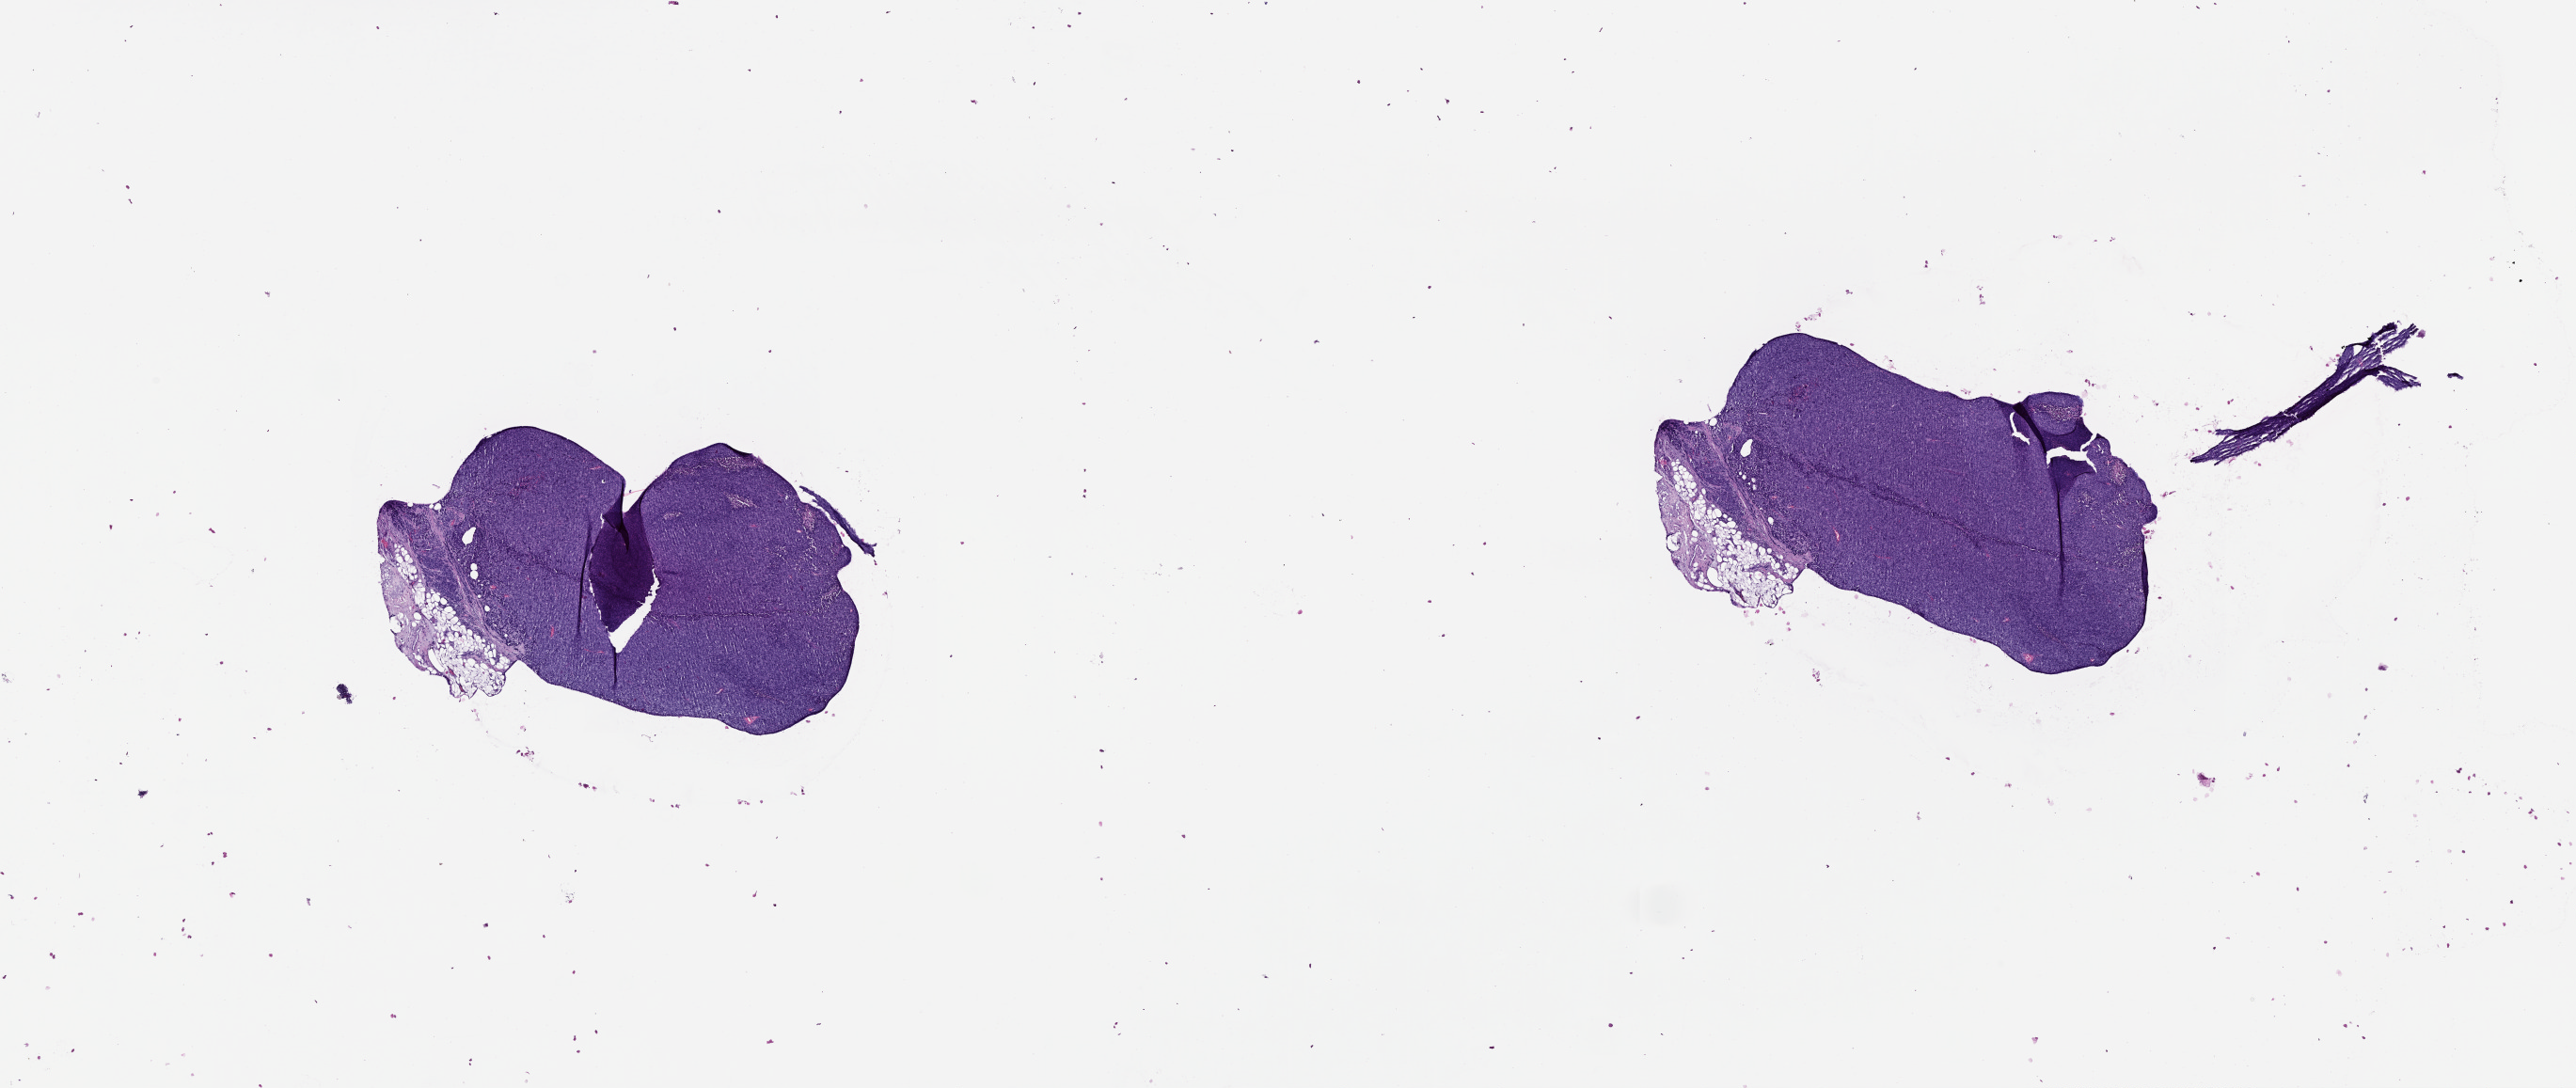
Whole-slide histology image, H&E — whole scanned area (about 22.0 x 9.3 mm, from a 20x scan) shown as a low-resolution overview, tumour tissue sample, sampled site: lymph node. Male, 53 y/o. Composition of this section per pathologist review: tumour nuclei 80%, necrosis 0%.
This section: metastatic tumour tissue. Patient diagnosis: Malignant melanoma, NOS.